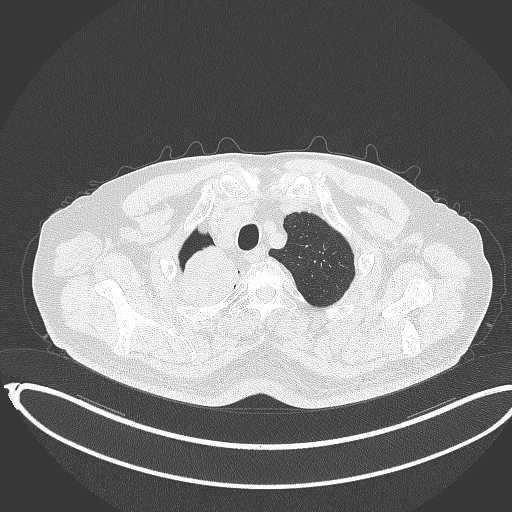
Chest CT, one axial slice. Slice 328 of 403 in the series (ordered by position). Lung window (W 1500 / L -600 HU). 1 mm slice thickness. 512 × 512 image matrix, field of view 436 × 436 mm. Male patient, age 68 years. Case-level facts recorded for this patient, not image findings: clinical TNM (as recorded): T2a N0 M0.
Structures marked on this image (bounding box drawn by a radiologist):
- lung tumour (recorded histology: adenocarcinoma): bounding box <176,242,249,308> (left, top, right, bottom; pixels)